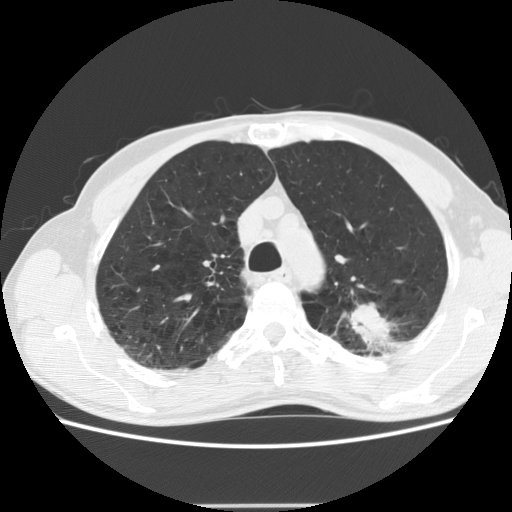
Low-dose screening chest CT, one axial slice; position 146 of 191 along the scan axis; reconstruction kernel STANDARD; lung window (W 1500 / L -600 HU); 512 × 512 image matrix, field of view 352 × 352 mm.
Structures marked on this image (expert manual segmentation):
- lesion 1 (tumor, upper lobe of left lung): box from (x=350, y=303) to (x=391, y=346) px